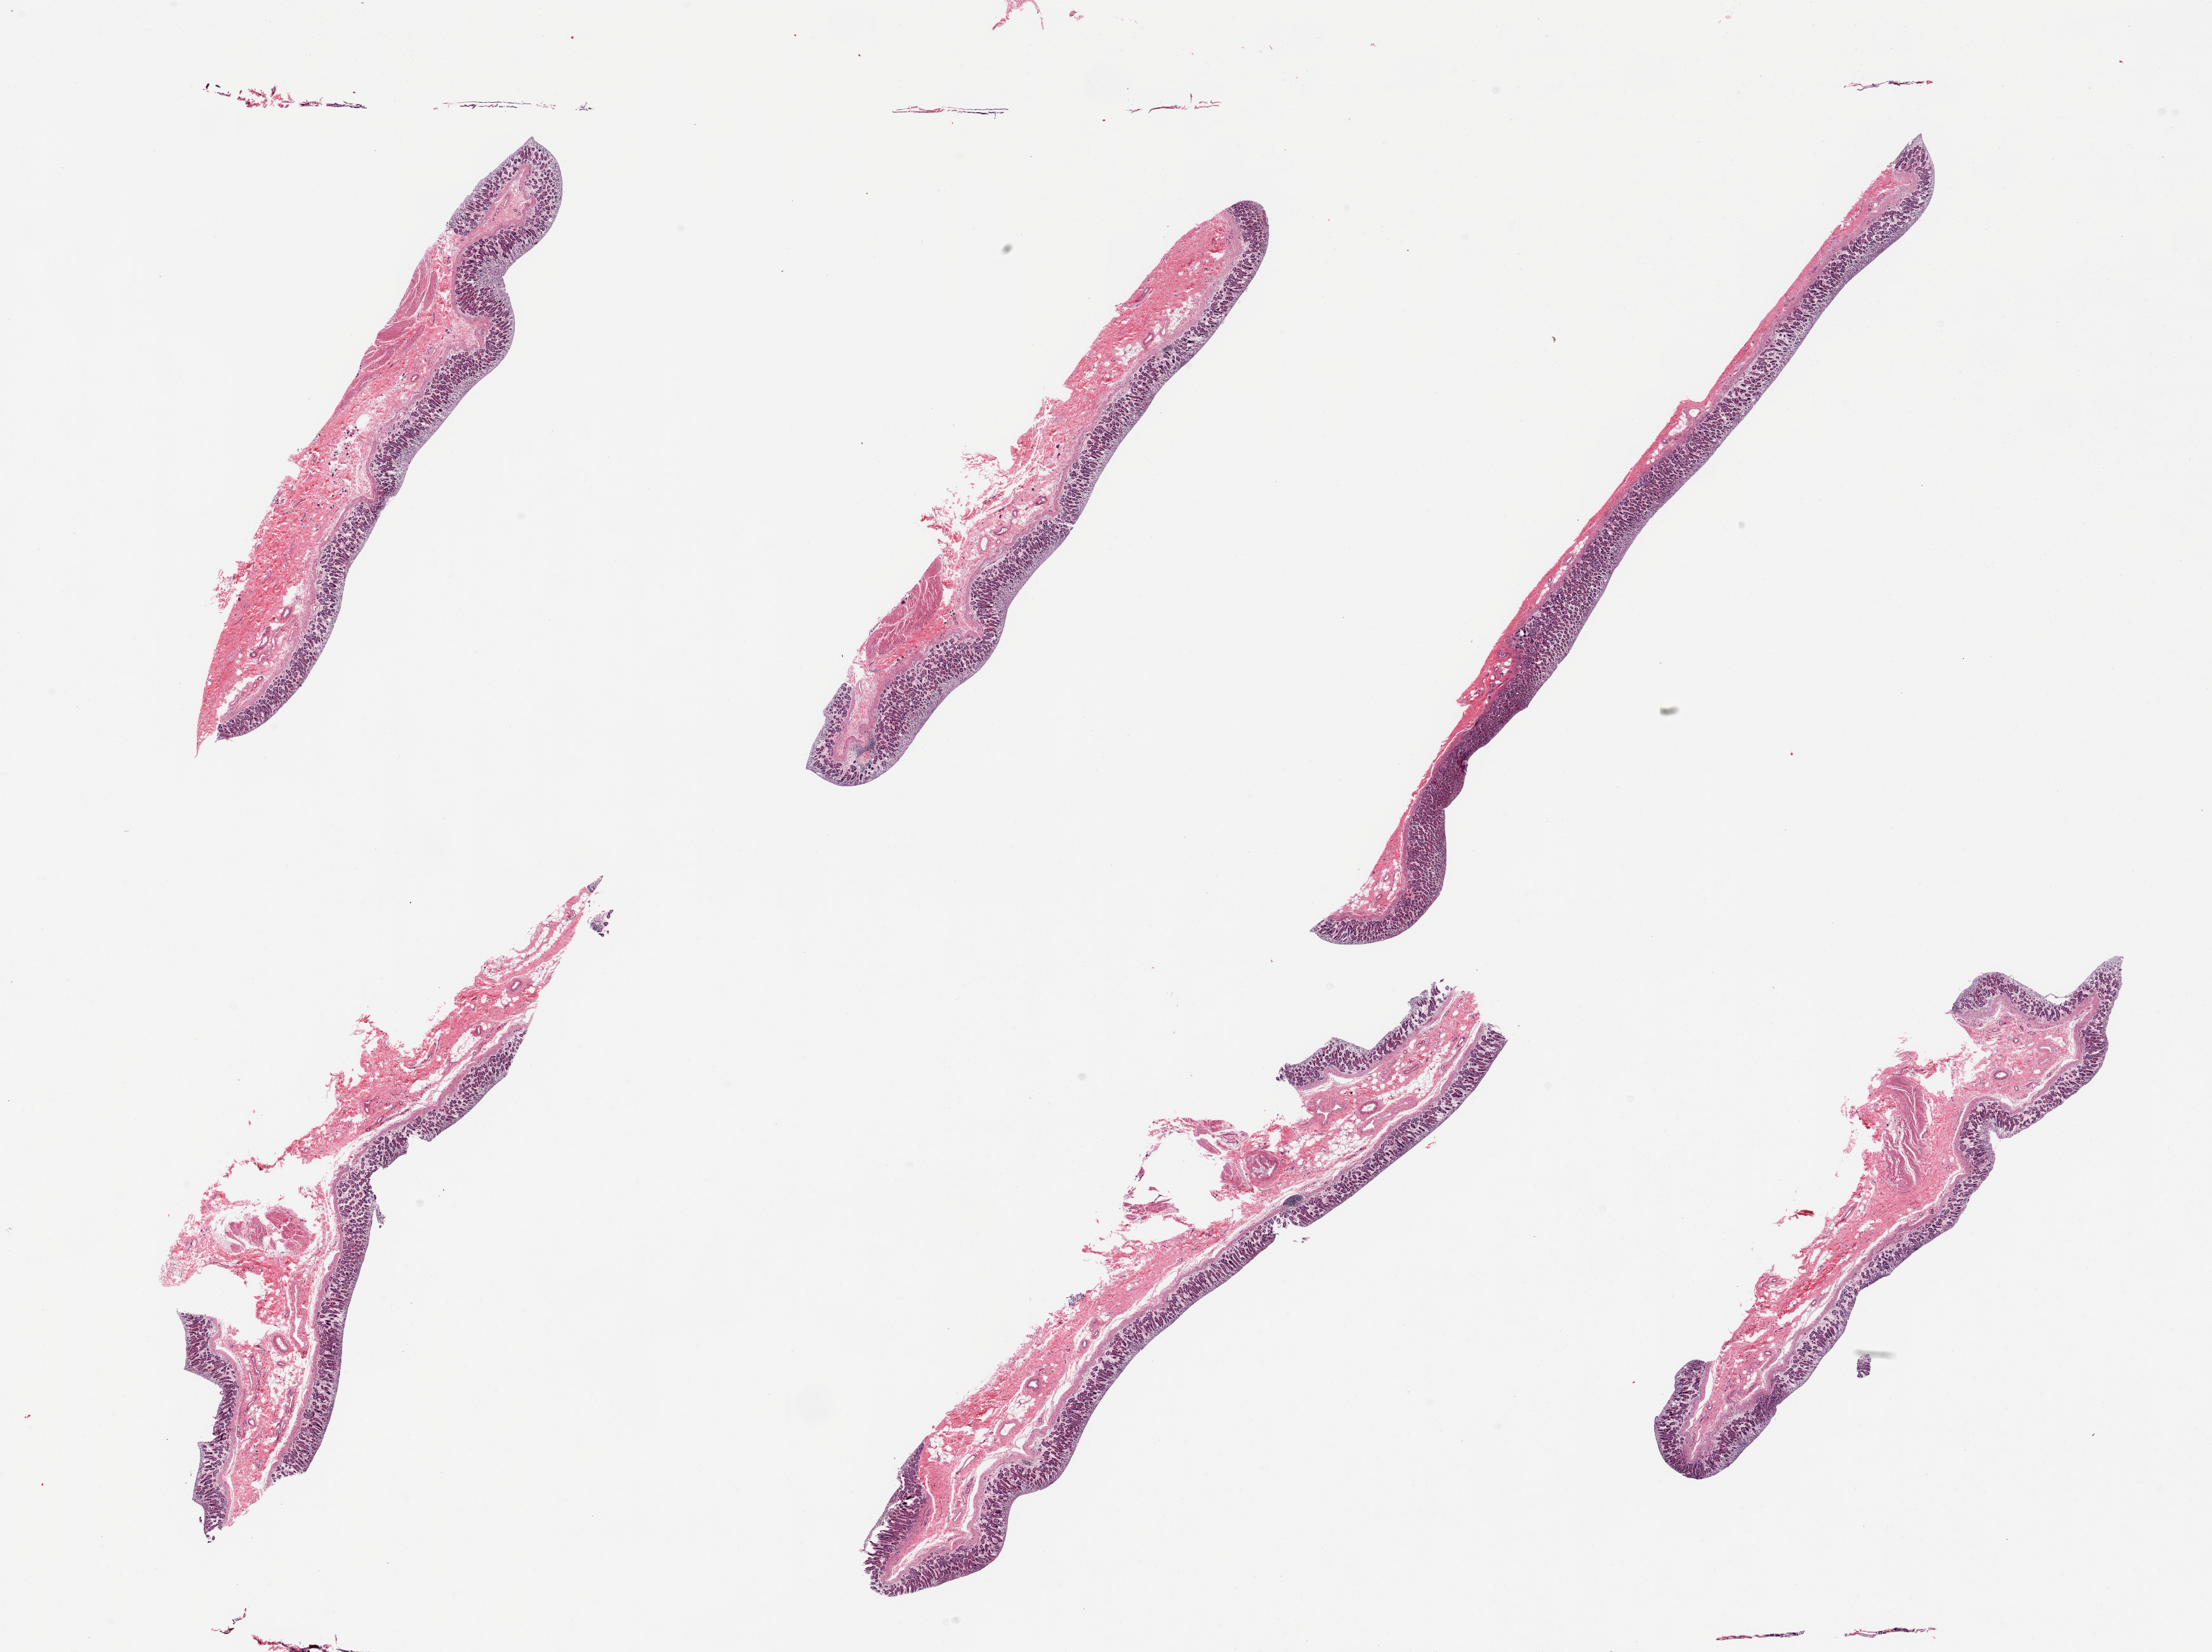
Hematoxylin and eosin (H&E) whole-slide image — whole scanned area (about 27.6 x 20.6 mm) shown as a low-resolution overview. PAXgene-fixed paraffin-embedded (PFPE) section. Sampled site (target tissue): stomach. Tissue donor sample. Donor sex: female.
* review note (as recorded): 6 pieces; autolyzed mucosa grade 1 focally approaching grade 2; in submucosa scattered crystalline deposits without a reaction, resemble resins; little or no muscularis present